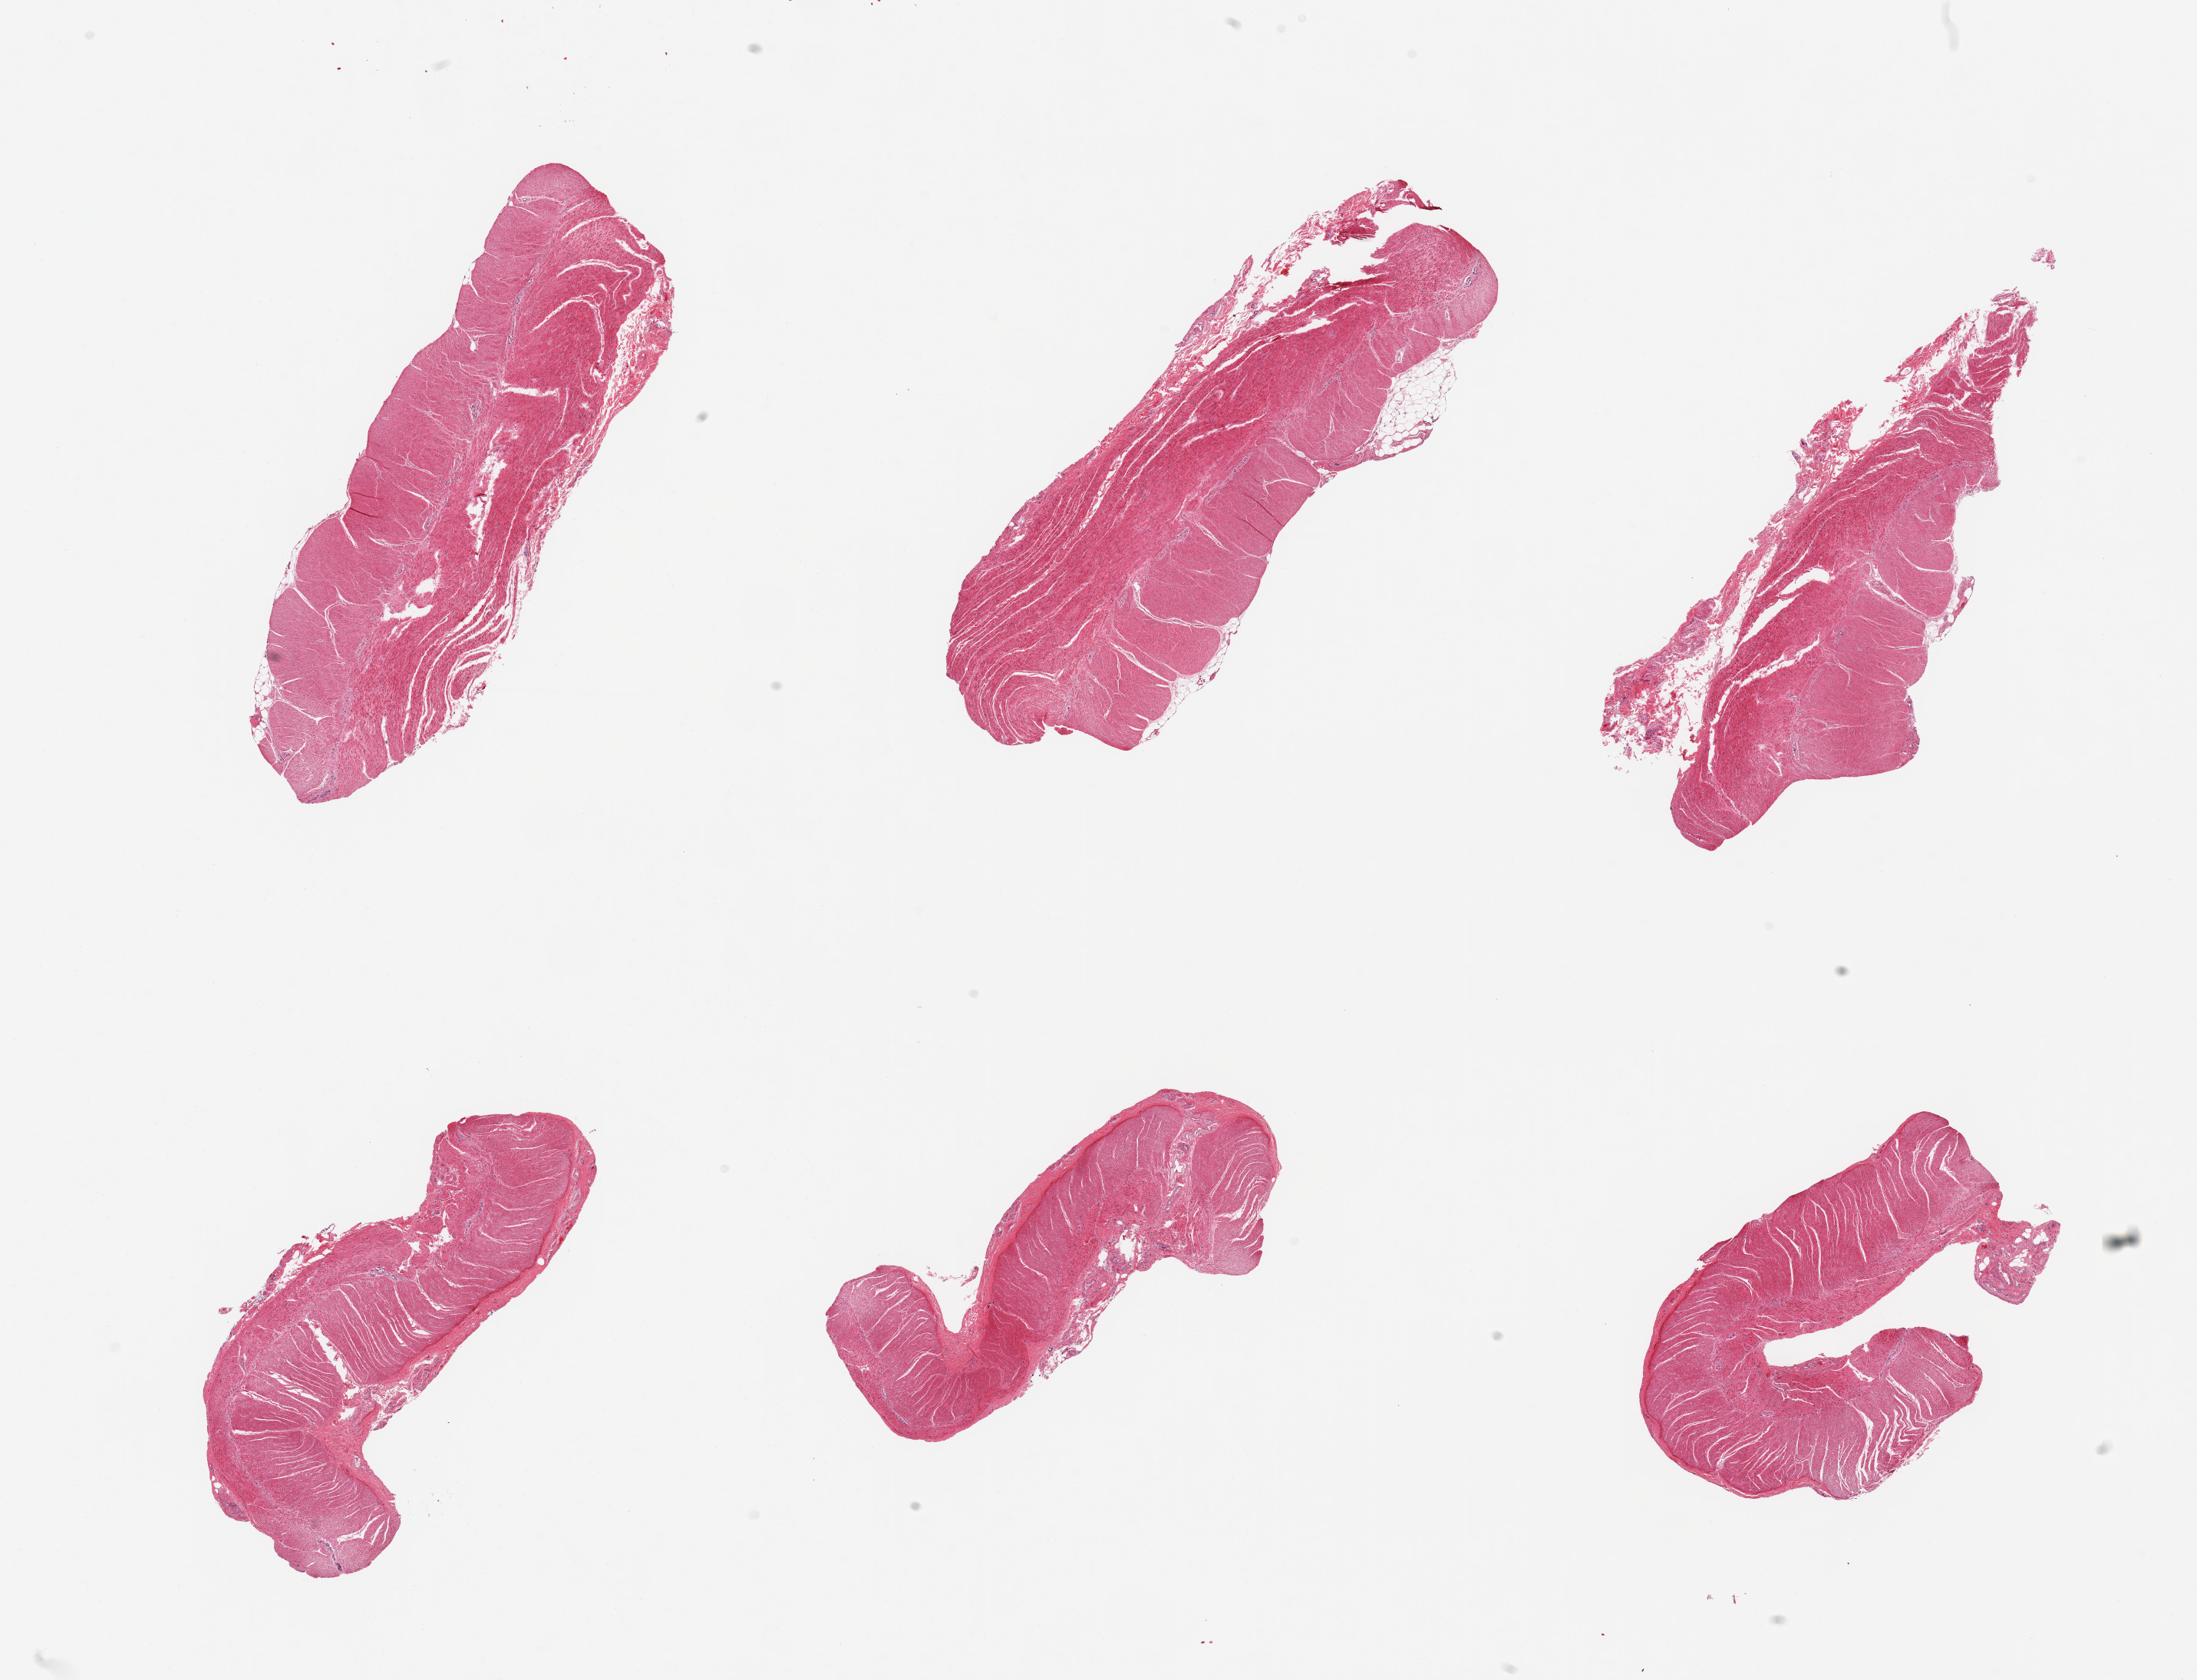
Digitized H&E-stained section — a low-resolution overview of the entire scanned area, about 22.6 x 17.3 mm. PAXgene-fixed paraffin-embedded (PFPE) section. Sampled site (target tissue): sigmoid colon. Tissue donor sample. Donor: male.
Pathologist's review note for this sample: 6 pieces, confirmed target muscularis.